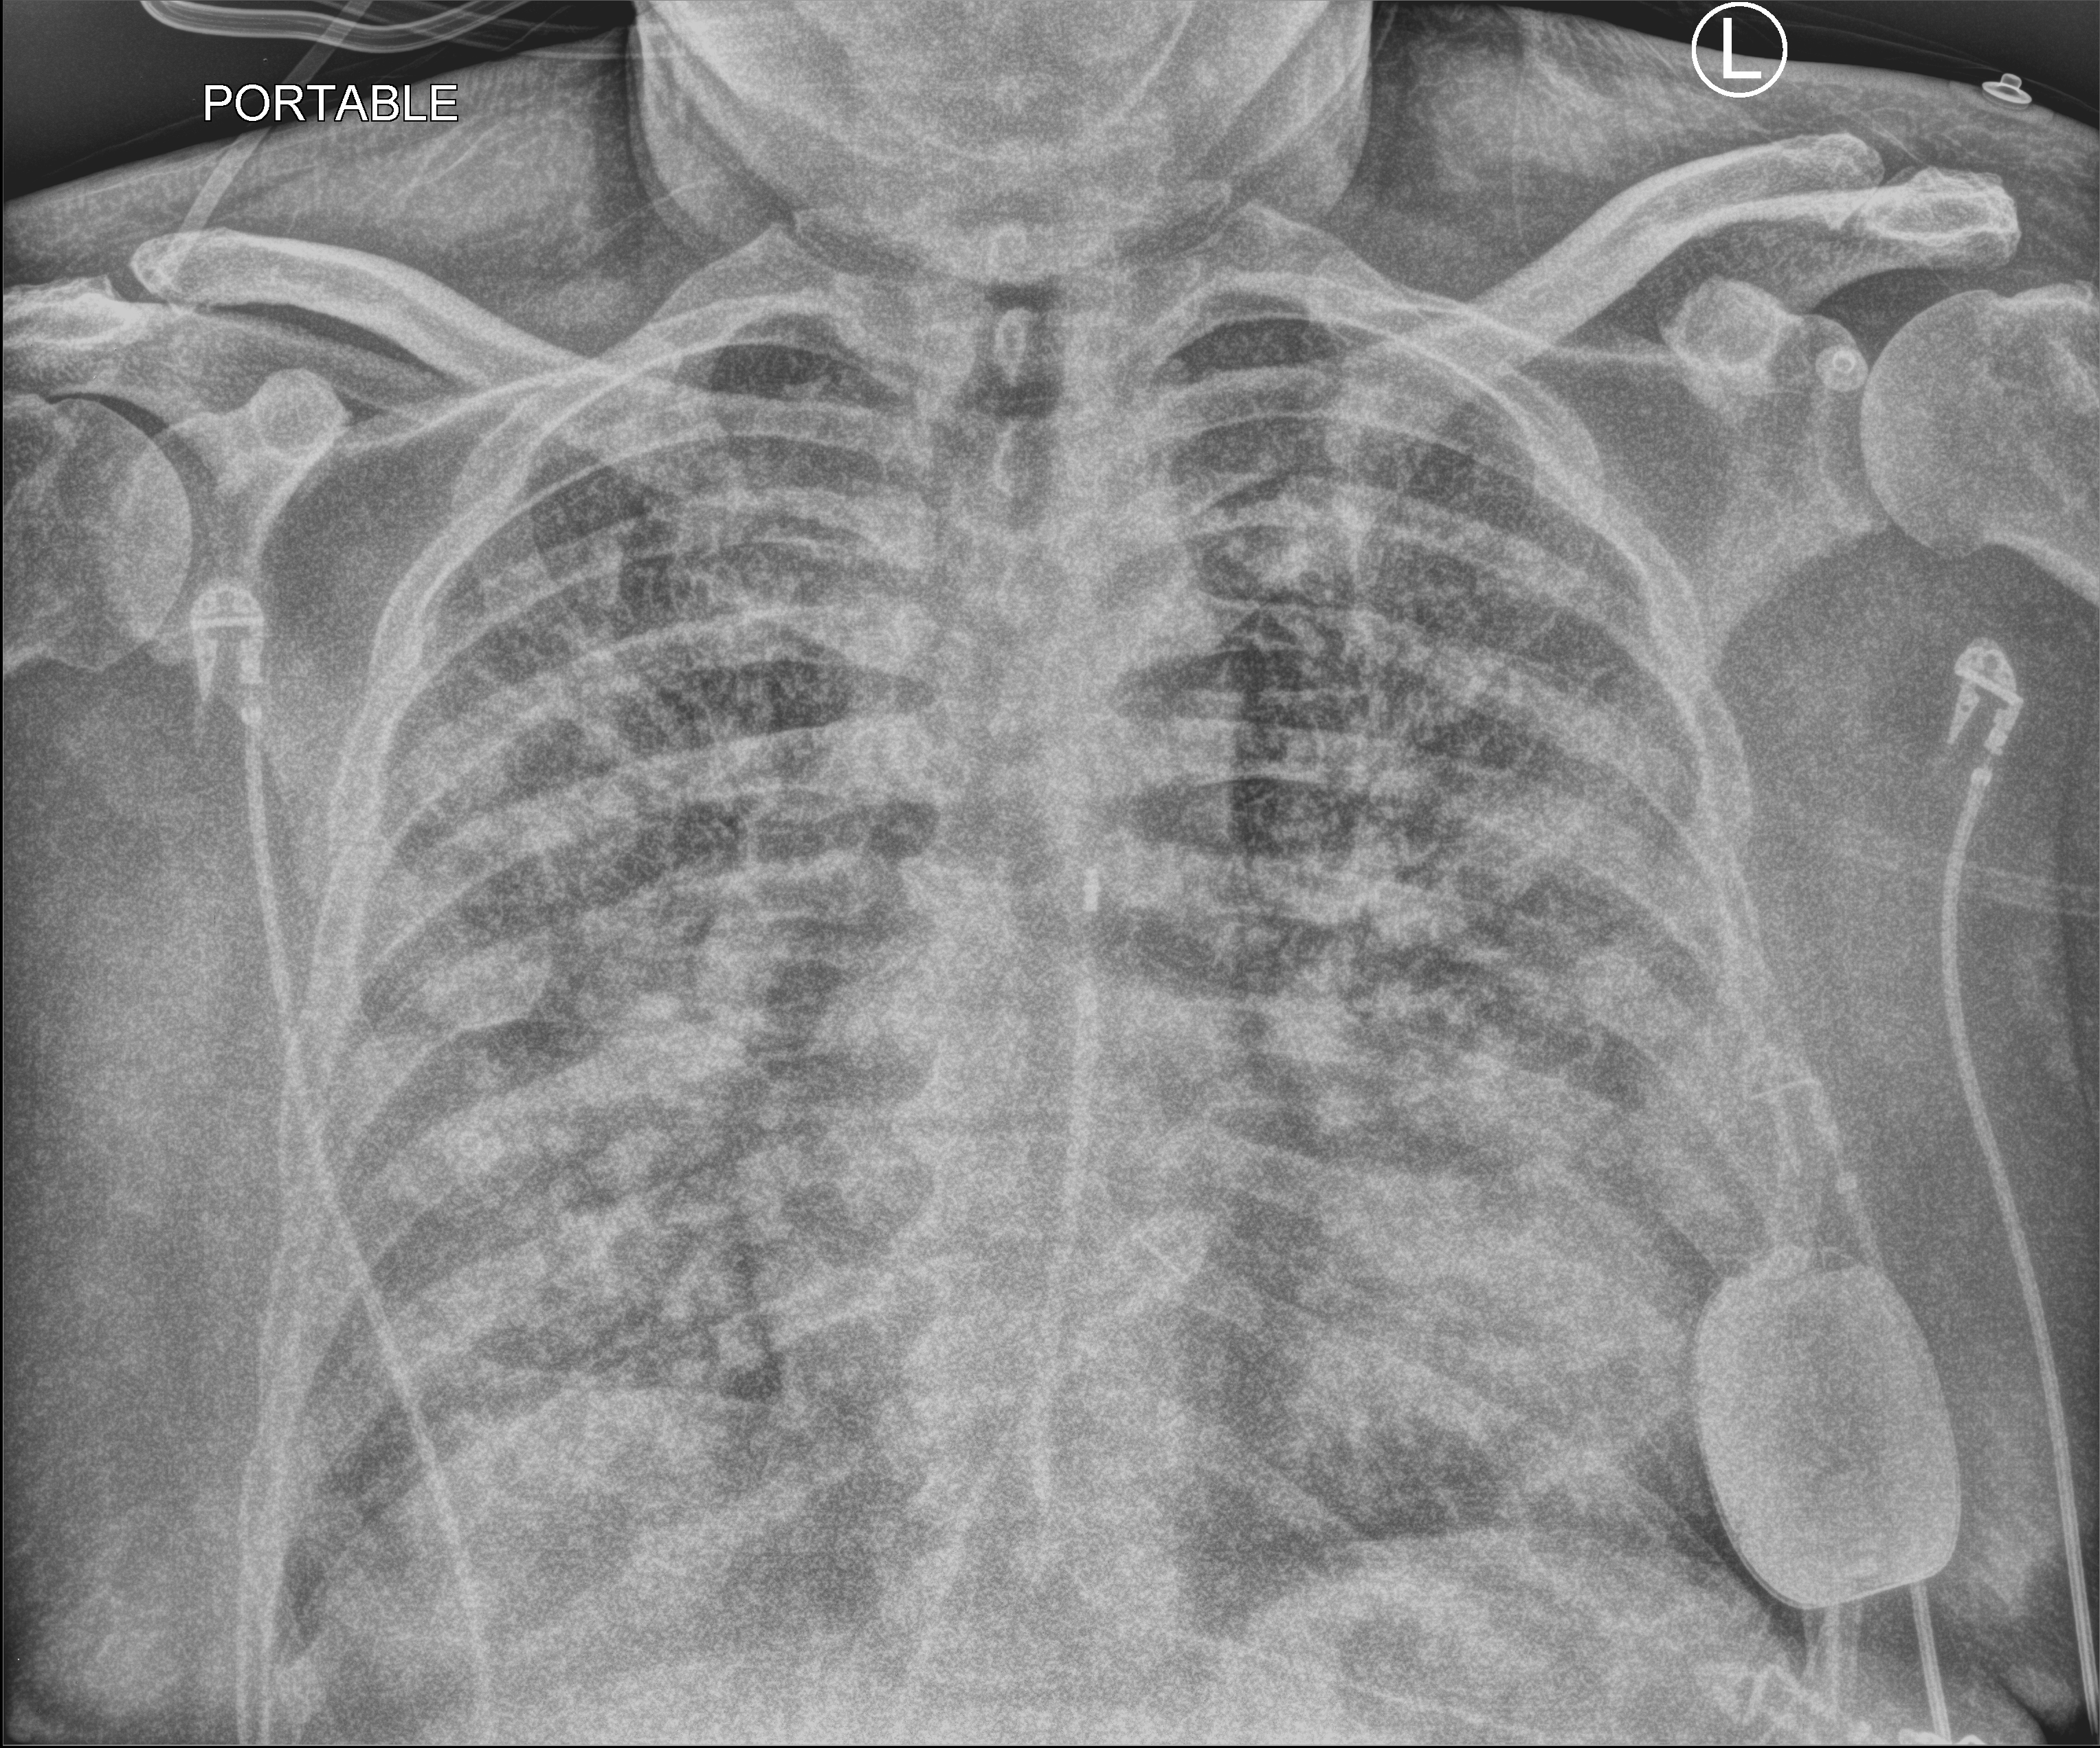
Portable chest radiograph; anteroposterior (AP) projection. Male patient hospitalised with COVID-19, age 60–74 years.
Admission-level facts for this patient (not findings on this image; timing relative to this image not recorded): mechanically ventilated during this hospital stay: yes.